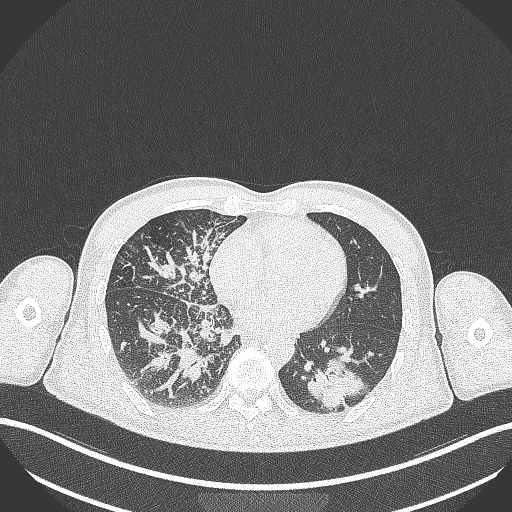
Chest CT, one axial slice; slice 122 of 348 in the series (ordered by position); reconstruction kernel B70f; 120 kVp; lung window (W 1500 / L -600 HU); 1 mm slice thickness; 512 × 512 image matrix, field of view 400 × 400 mm. Male patient, age 49 years. Case-level facts recorded for this patient, not image findings: clinical TNM (as recorded): T2b N1 M0.
Structures marked on this image (bounding box drawn by a radiologist):
- lung tumour (recorded histology: adenocarcinoma): bounding box <305,358,369,408> (left, top, right, bottom; pixels)